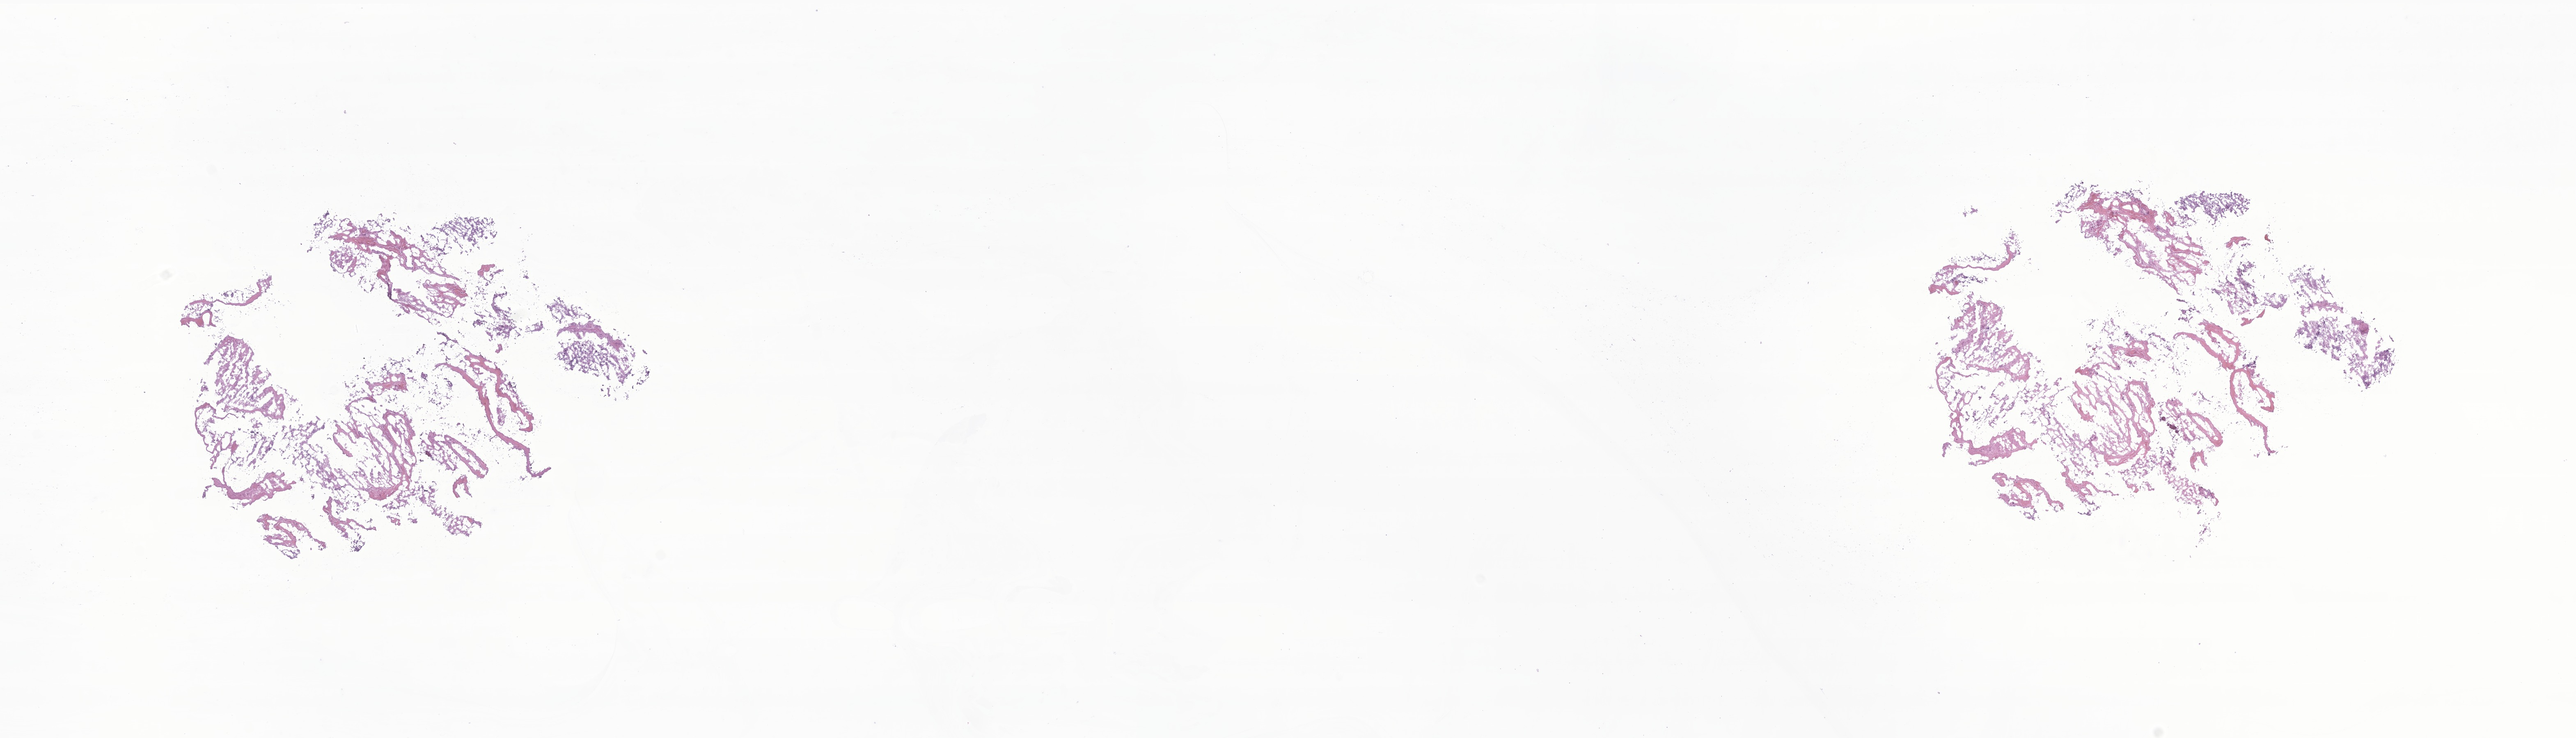
Whole-slide image, H&E stain of tumor tissue from the parietal lobe, whole scanned area (about 26.5 x 7.6 mm) shown as a low-resolution overview. Frozen section (OCT-embedded). Male patient, age 99 months.
- diagnosis: Glioblastoma, NOS